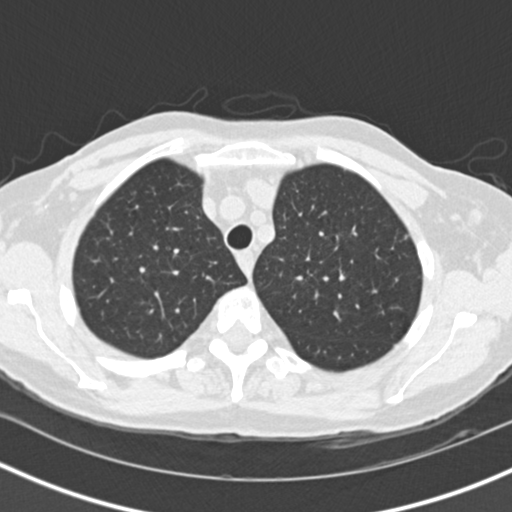
Axial slice from a low-dose chest CT screening exam; first (baseline) screen; lung window (W 1500 / L -600 HU); 2 mm slice thickness; standard (soft-tissue) reconstruction kernel (B30f). Female participant, aged 73 years at enrolment.
- Expert-annotated lung lesion, box from (x=316, y=208) to (x=371, y=276) px.
- Reader record for this screening exam (exam-level; its link to the box is not recorded): non-calcified nodule or mass ≥4 mm, left upper lobe, 27 × 21 mm, spiculated (stellate) margins, soft tissue attenuation.
- Official screen result: positive, change unspecified: nodule(s) >= 4 mm or enlarging nodule(s), mass(es), or other non-specific abnormalities suspicious for lung cancer.
- Lung cancer was diagnosed 72 days after this screen: bronchiolo-alveolar adenocarcinoma, NOS, left upper lobe, moderately differentiated (G2), stage IIIB (AJCC 6th edition), 17 mm at pathology.